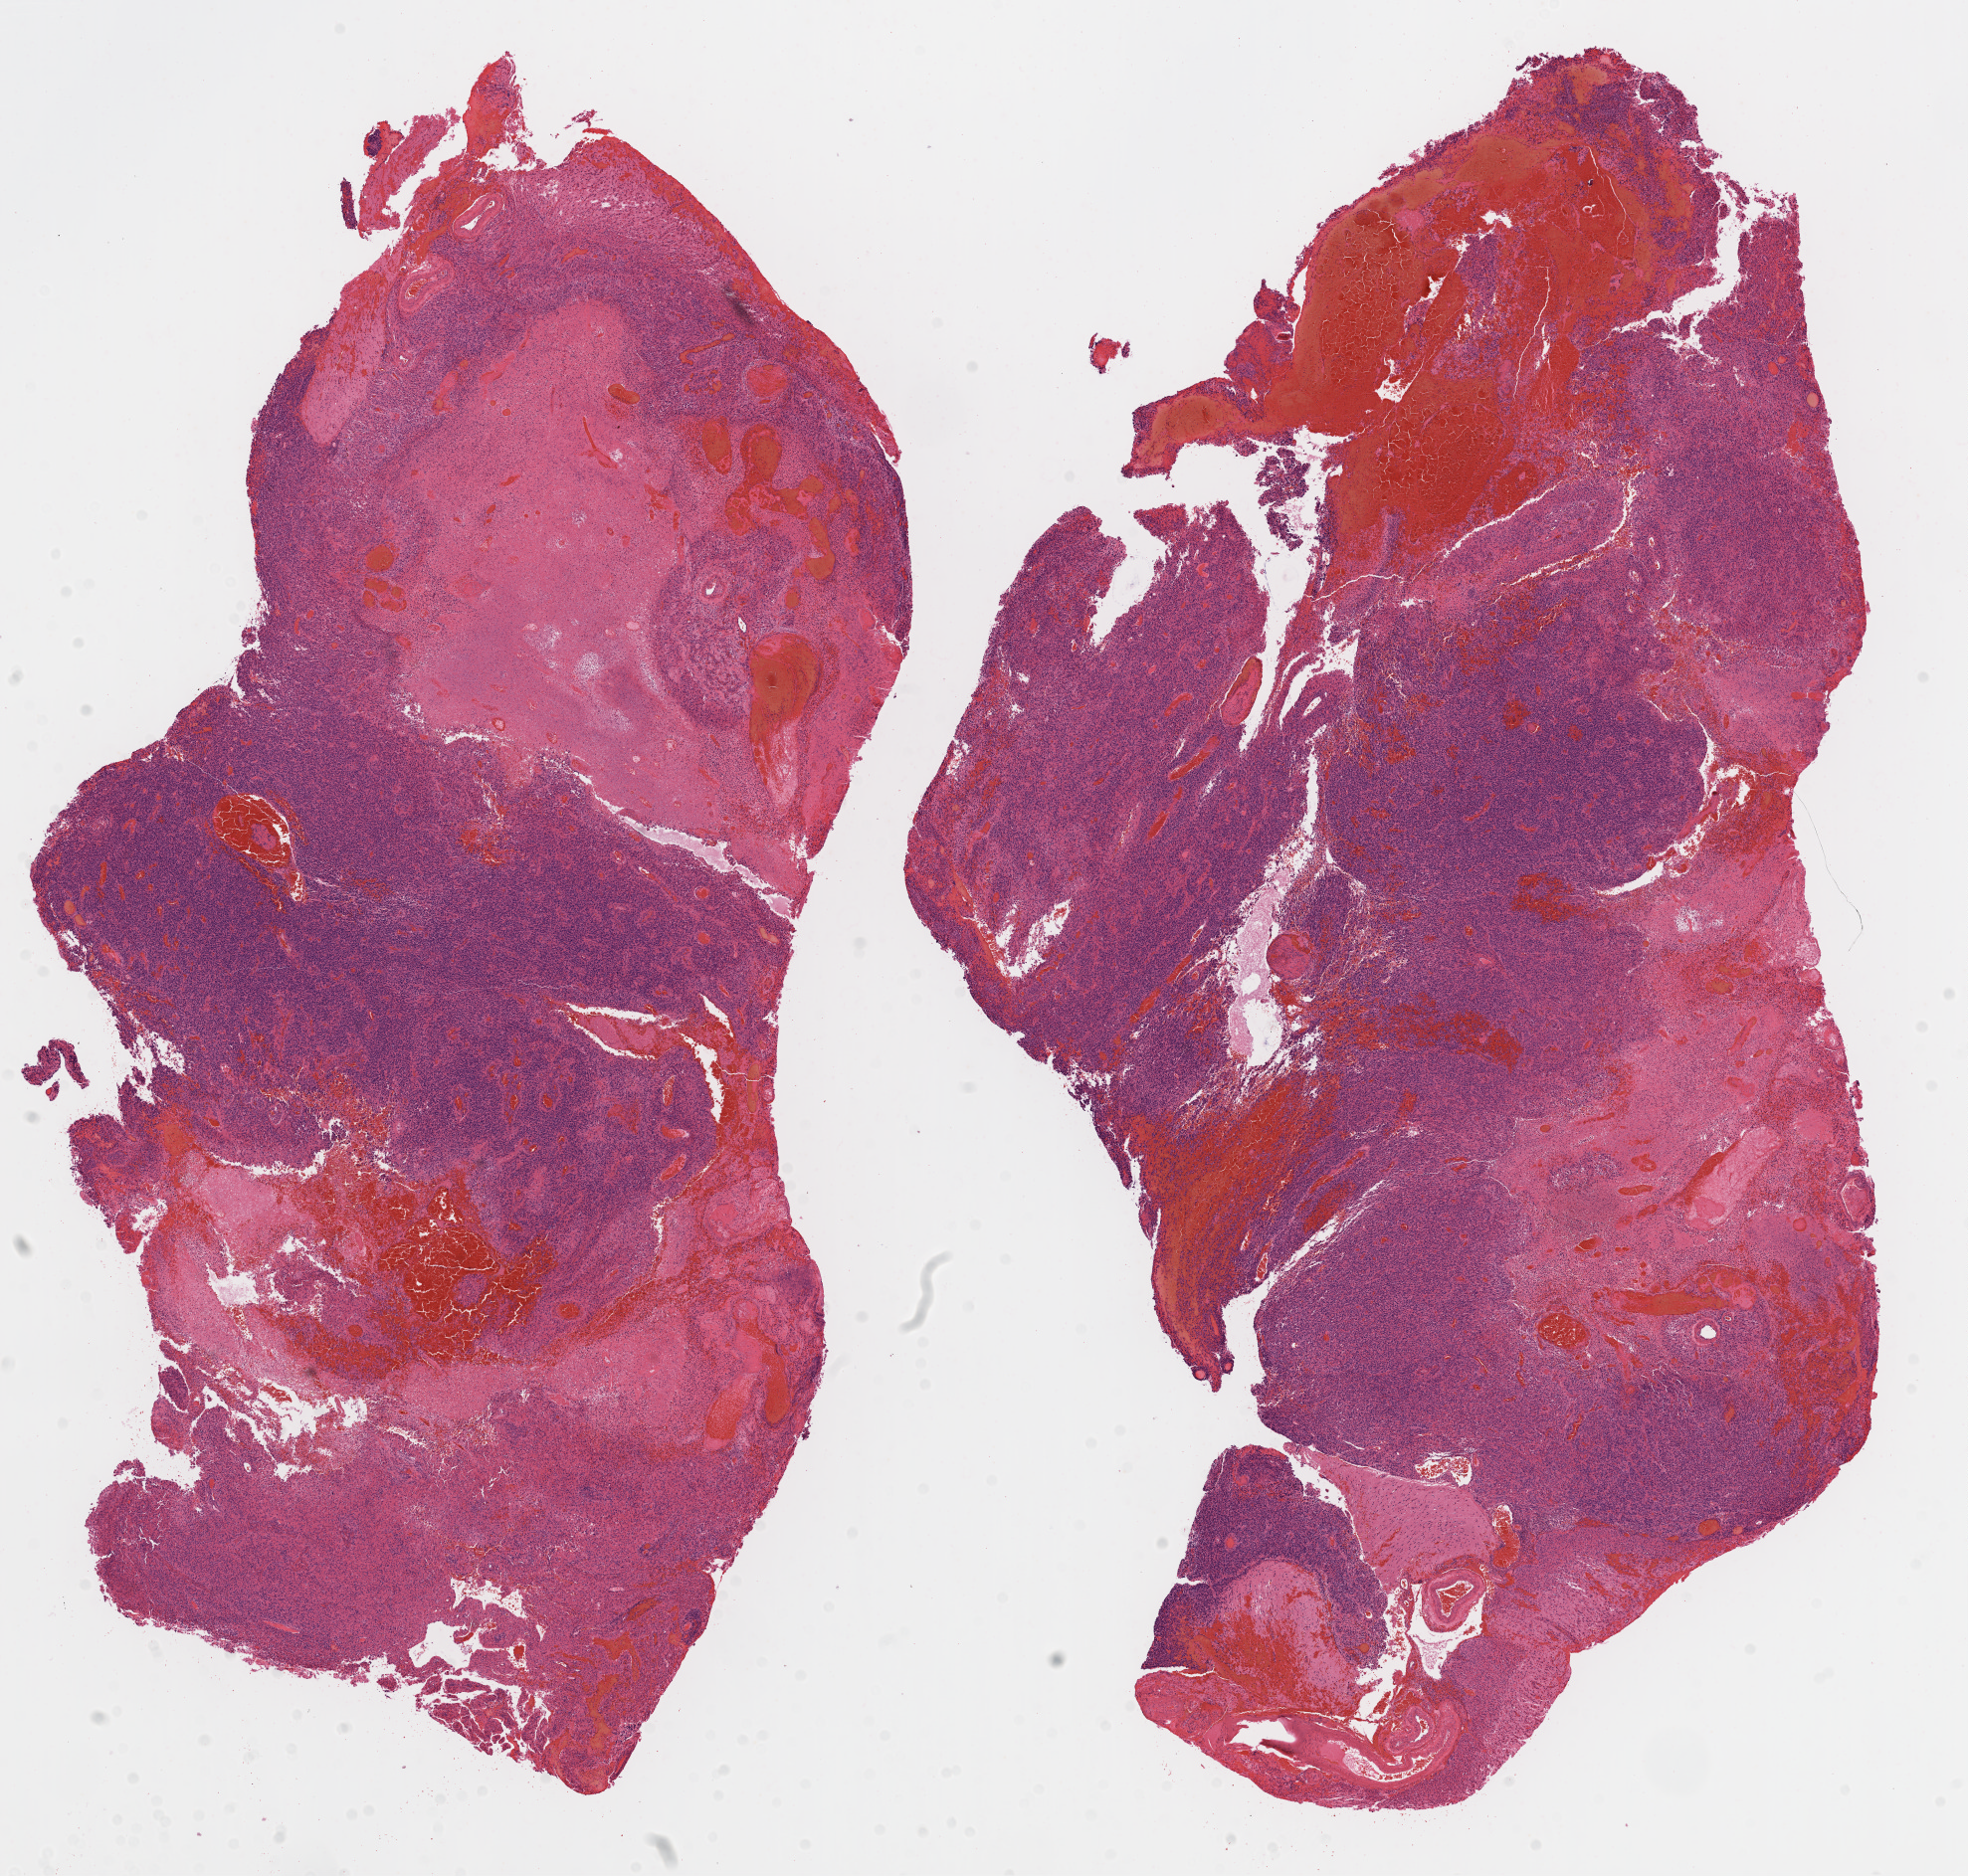
Digitized H&E-stained tissue section (whole slide) — shown as a low-resolution overview of the whole scanned area (about 16.0 x 15.2 mm). Formalin-fixed paraffin-embedded (FFPE) diagnostic section. Brain, primary tumour sample. Female, age 61 years at initial diagnosis.
Diagnosis: Glioblastoma.